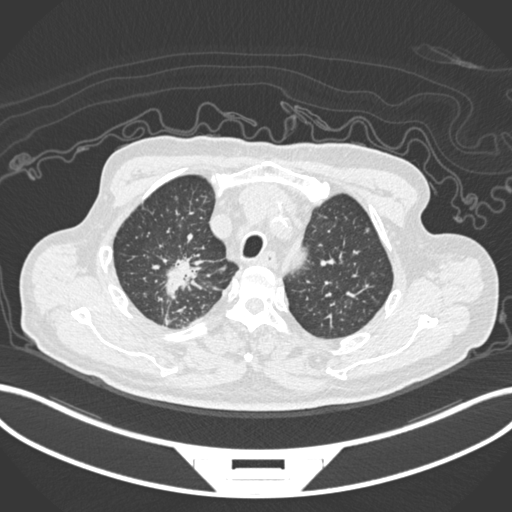
Chest CT, one axial slice; position 173 of 207 along the scan axis; 120 kVp; lung window (W 1500 / L -600 HU); 1 mm slice thickness; 512 × 512 image matrix, field of view 400 × 400 mm. Male patient, age 69 years. Case-level facts recorded for this patient, not image findings: clinical TNM (as recorded): T1c N1 M1.
Annotated regions visible in this slice (bounding box drawn by a radiologist):
- lung tumour (recorded histology: adenocarcinoma): bounding box [x1, y1, x2, y2] px = [165, 252, 208, 300]